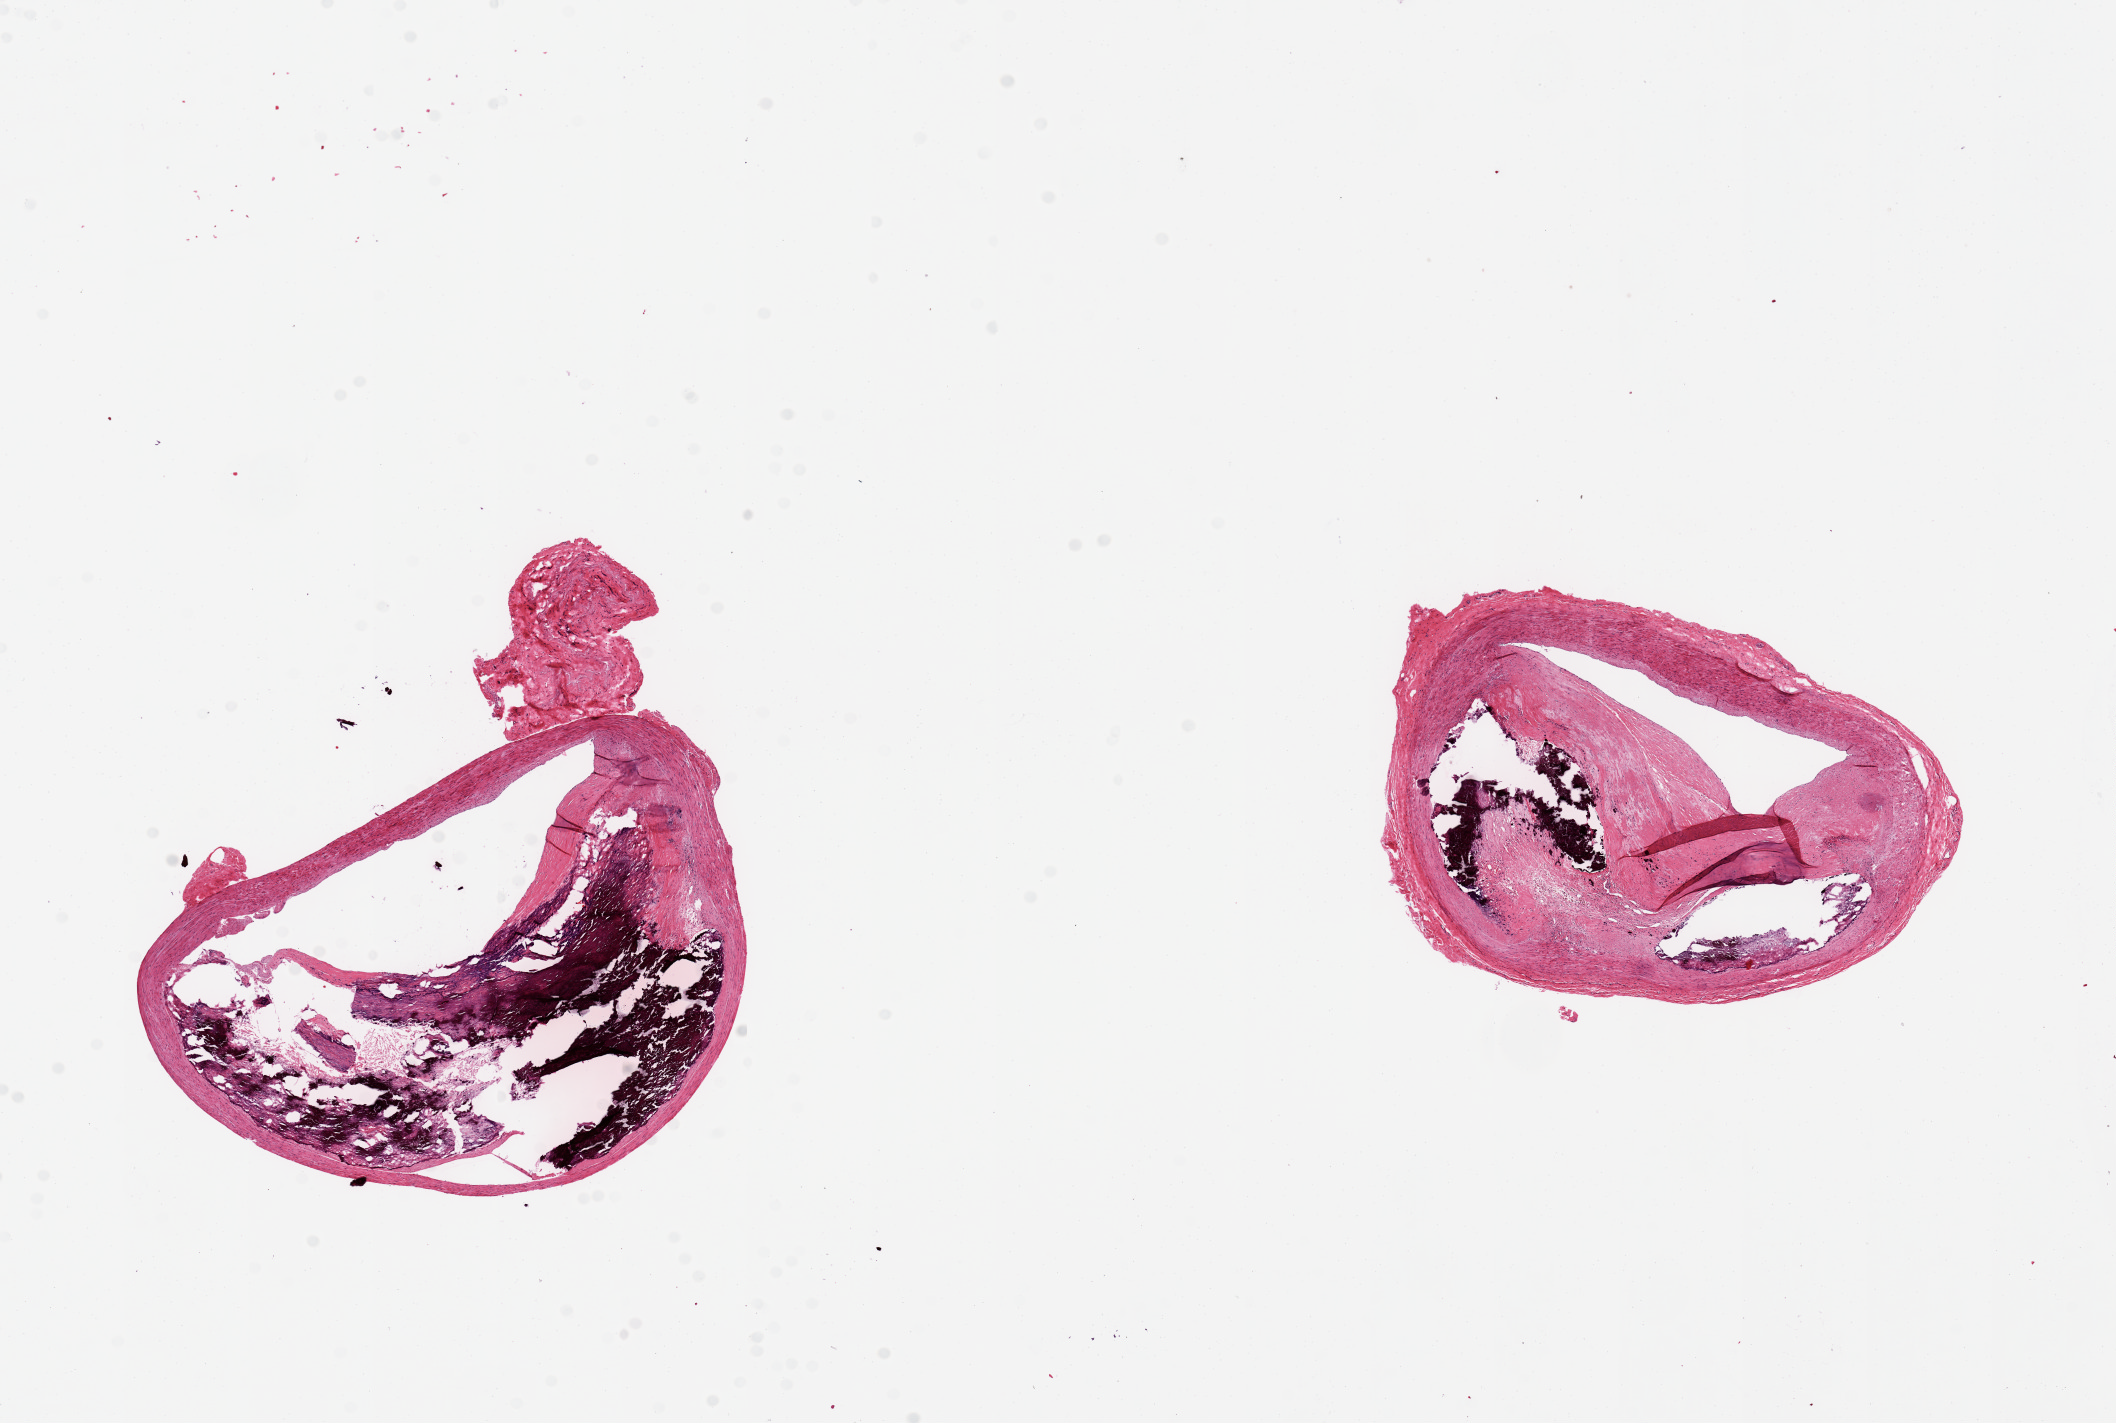
Digitized H&E-stained section, low-resolution overview of the scanned area, about 16.7 x 11.3 mm (acquisition: 20x scan). PAXgene-fixed, paraffin-embedded tissue. Section of coronary artery (target tissue). Tissue donor sample. Donor sex: male.
- reviewer comment on this tissue sample: 70% occlusive coronary artery disease, calcified